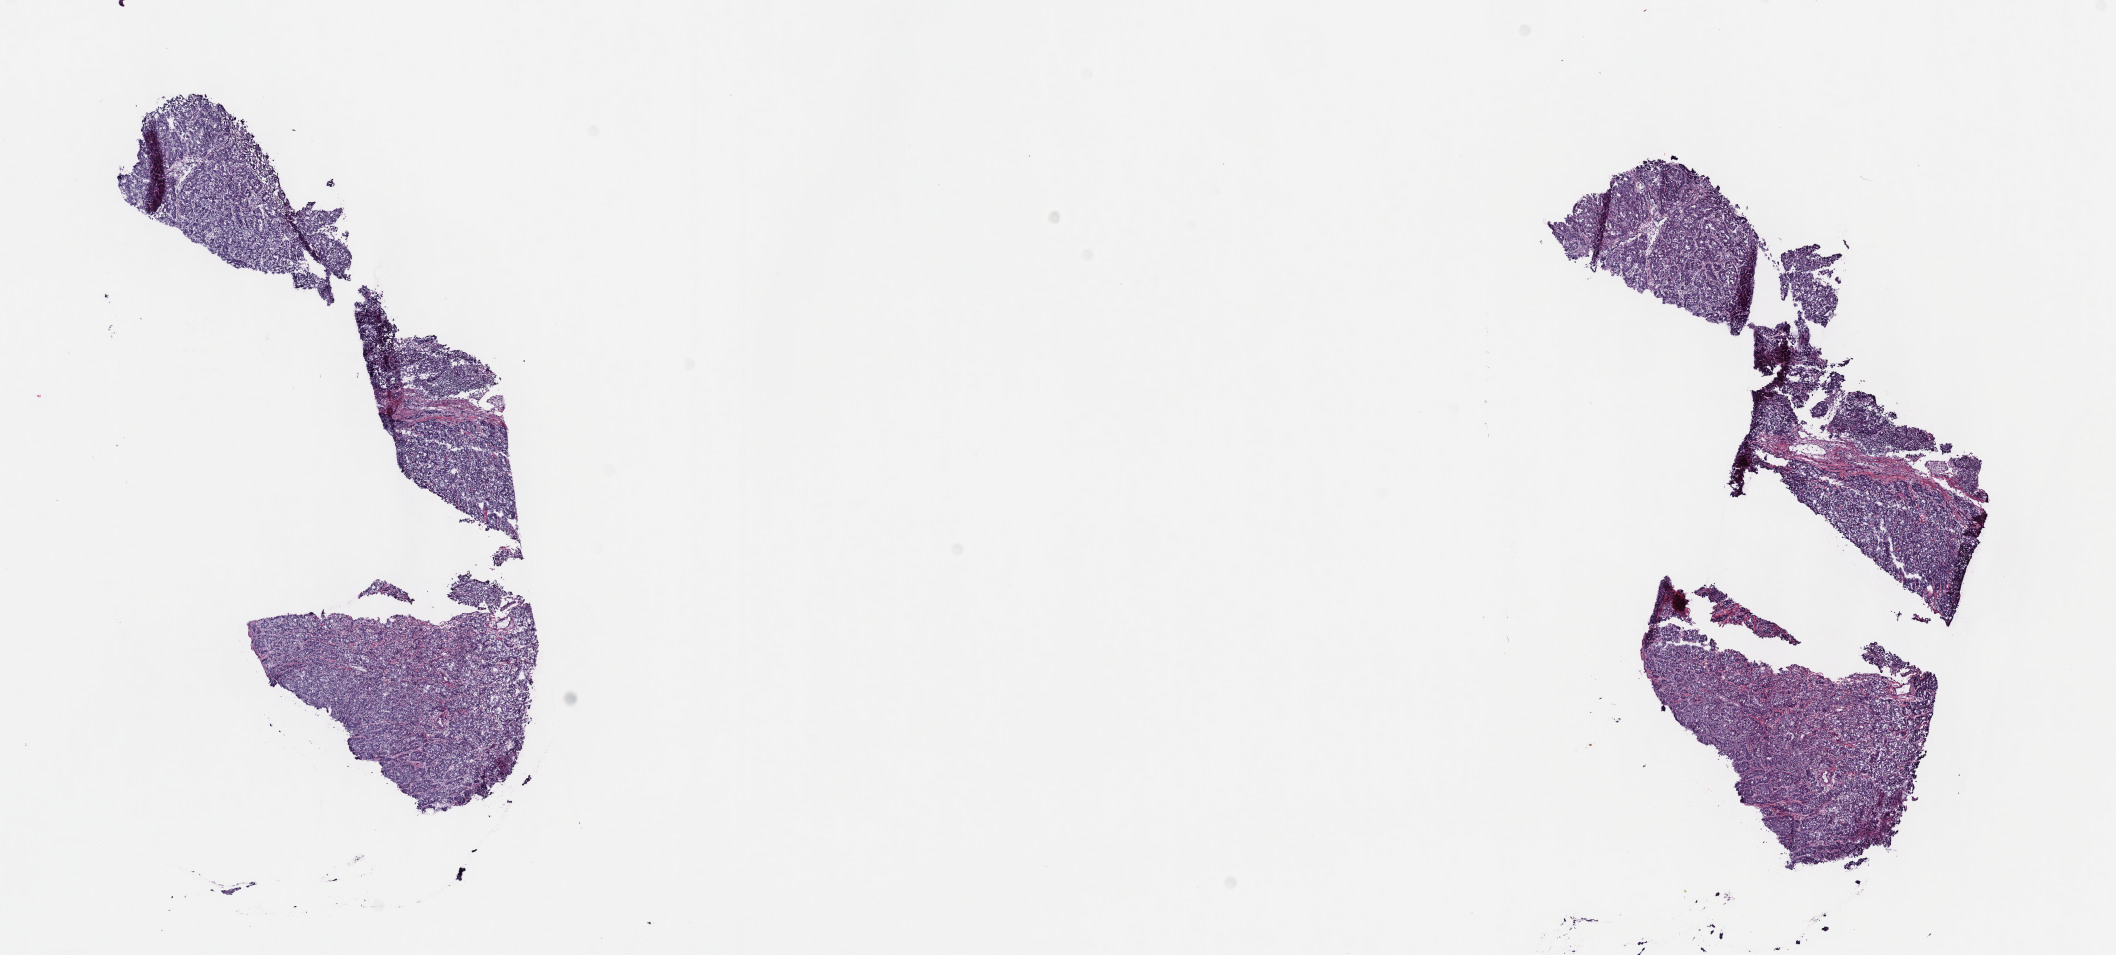
Digitized Hematoxylin and eosin (H&E) stained tissue section (whole slide), whole scanned area (about 17.1 x 7.7 mm) shown as a low-resolution overview. Frozen section from the top of the tissue portion. Lung, primary tumour sample. Male, age 41 years at initial diagnosis. Slide review estimates, as recorded: tumour cells 80%, tumour nuclei 80%.
Histologic diagnosis: Mucinous adenocarcinoma.